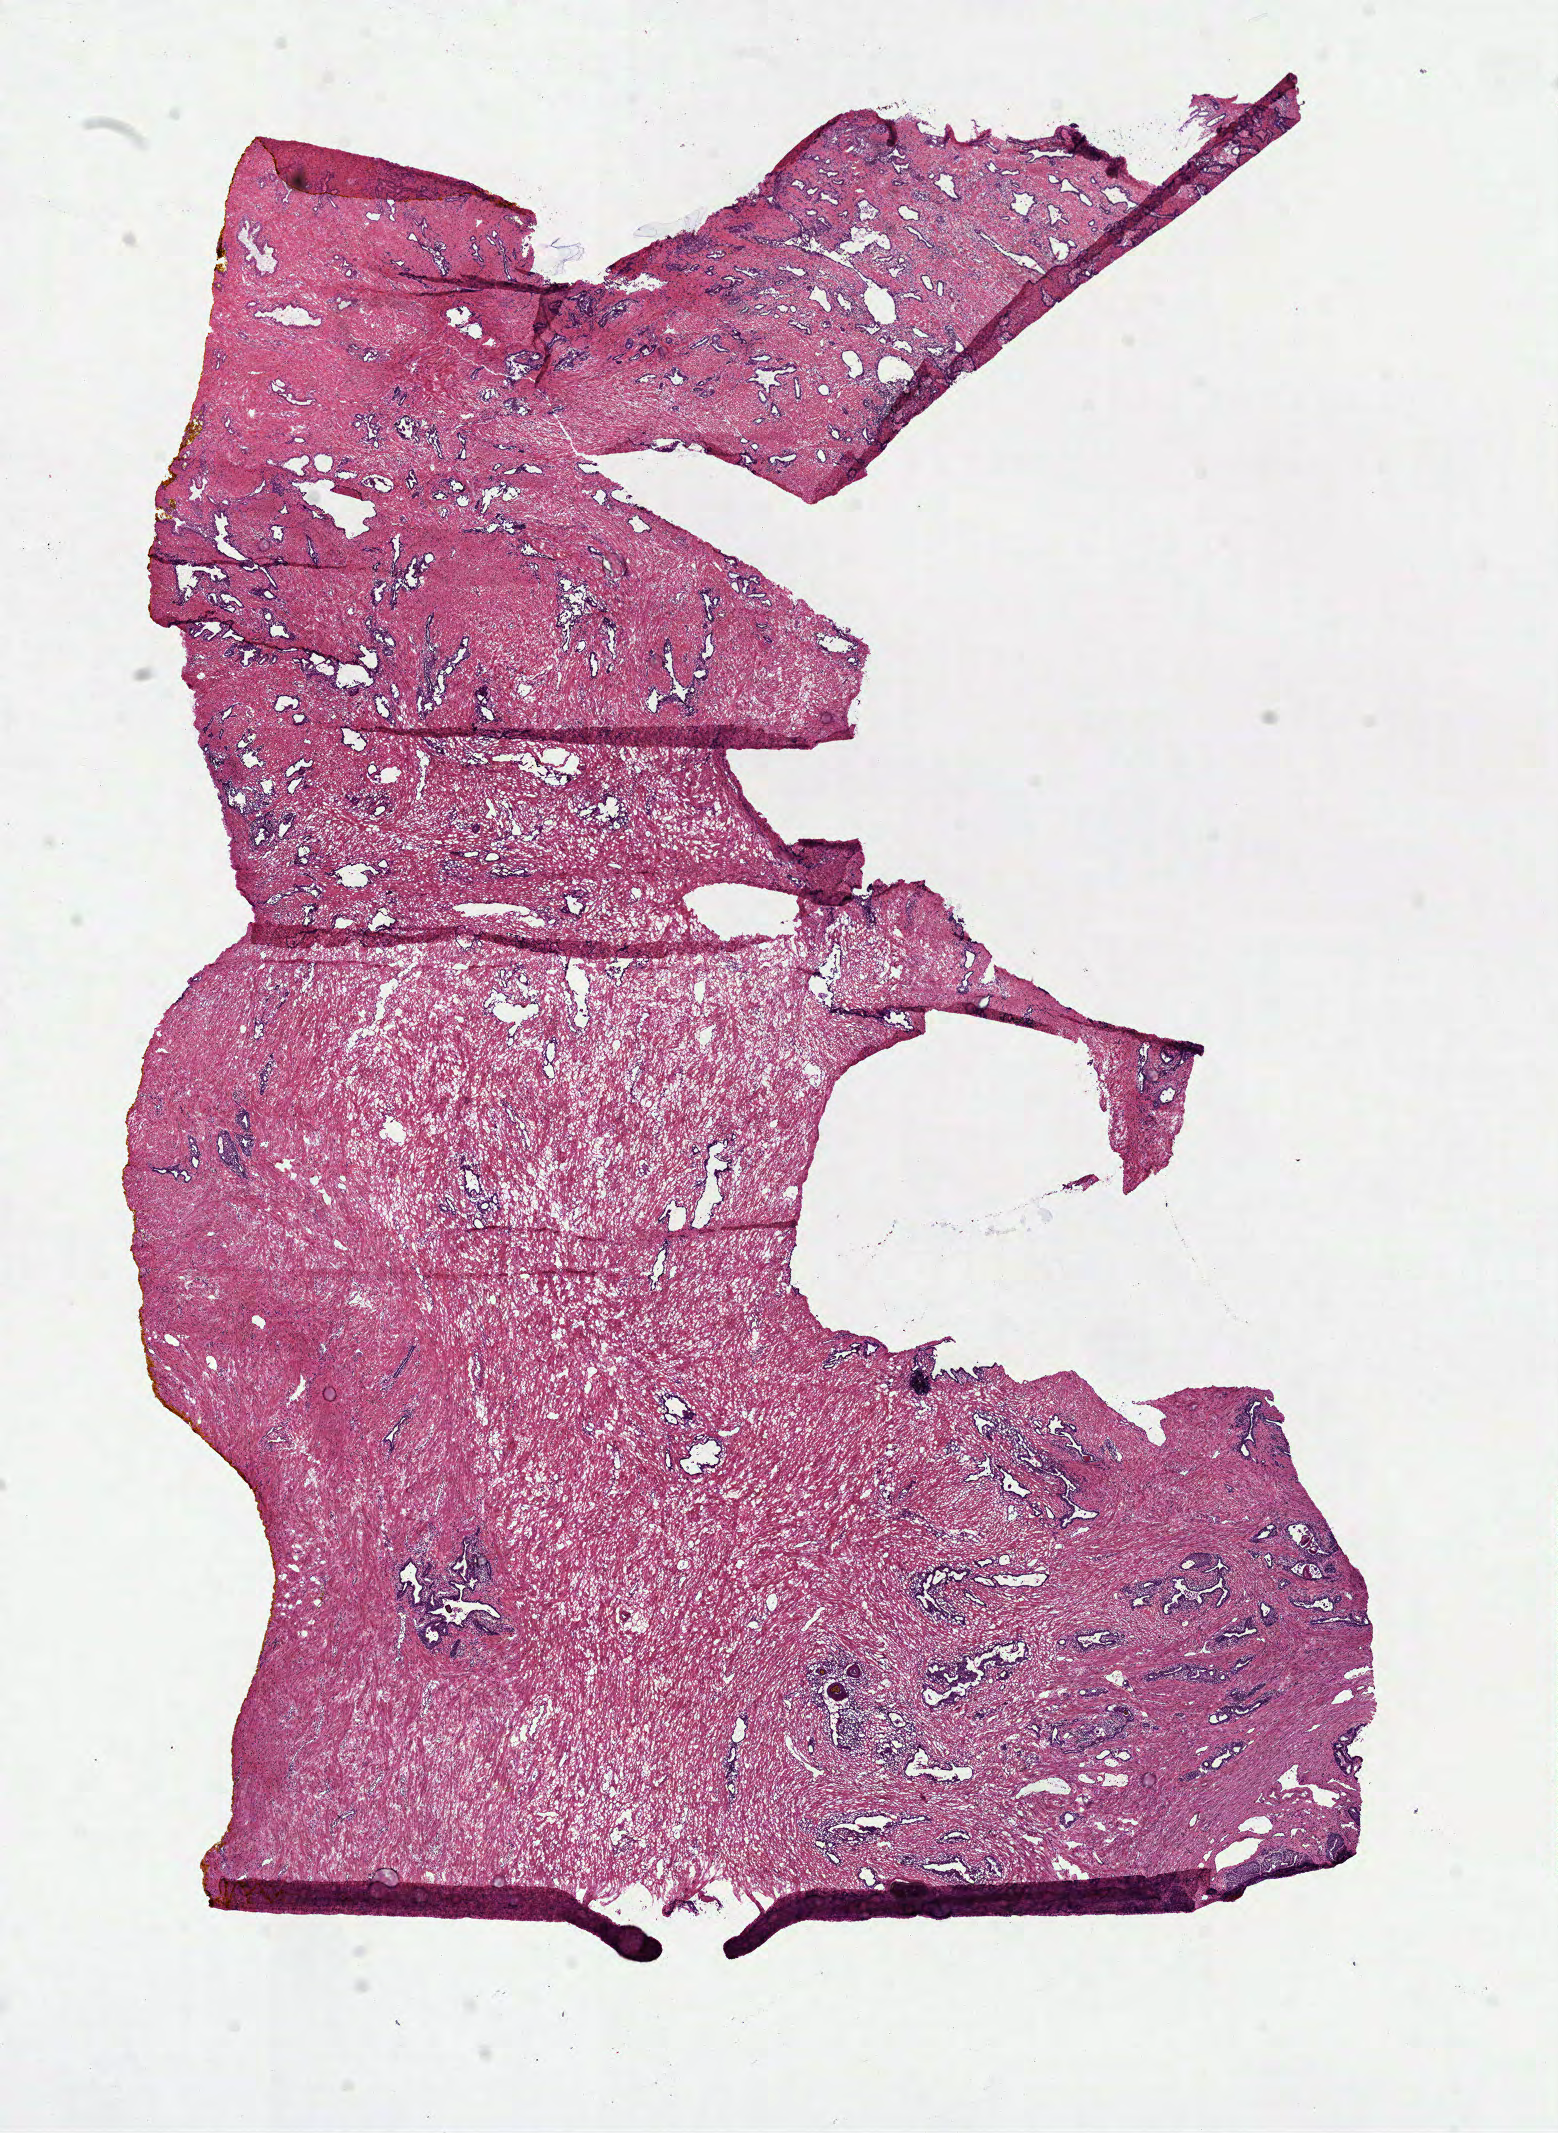
Whole-slide histology image, H&E, whole scanned area (about 12.6 x 17.2 mm, from a 40x scan) shown as a low-resolution overview; frozen section from the top of the tissue portion; sample: solid tissue normal (non-tumour tissue), prostate. Male, age 68 years at initial diagnosis.
This section: solid tissue normal (non-tumour) sample from the same patient. Patient diagnosis: Acinar cell carcinoma (prostate gland).